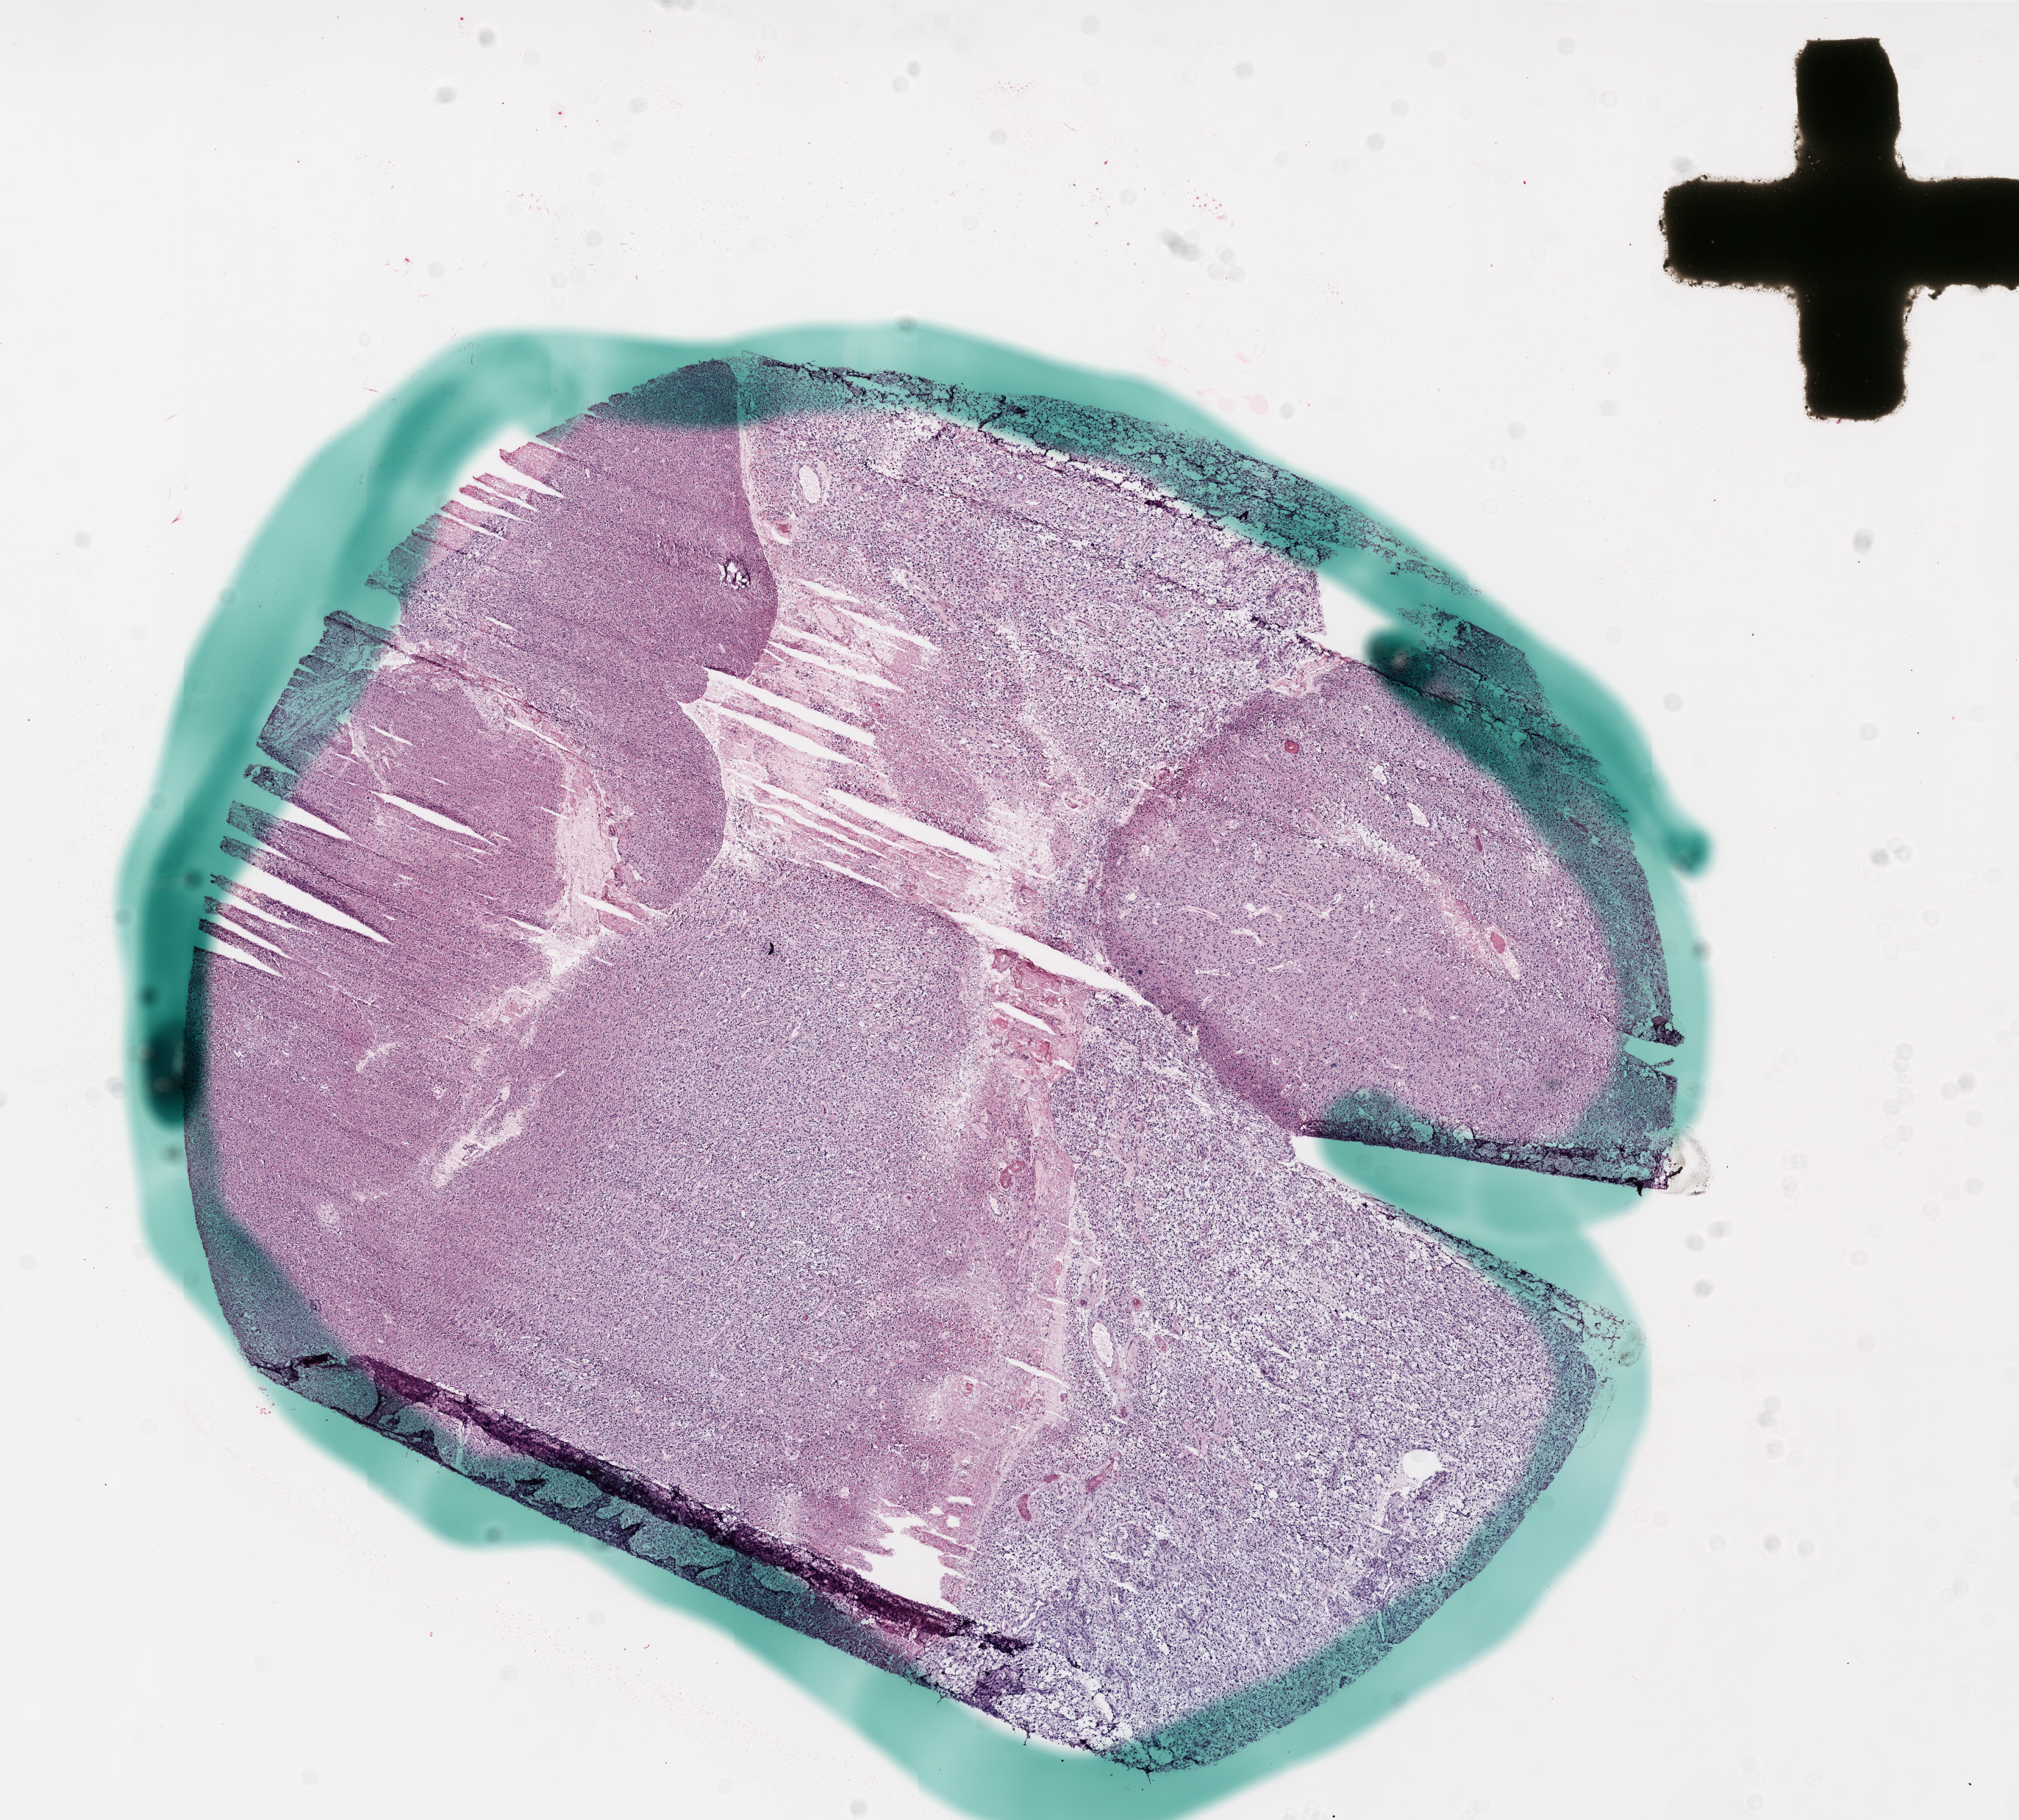
H&E whole-slide image, low-resolution overview of the scanned area, about 11.0 x 9.9 mm; frozen section; sample: primary tumour, brain. Male patient; age at initial diagnosis 67 years. Composition of this section per pathologist review: tumour cells 85%, tumour nuclei 95%, normal cells 5%, stromal cells 0%, necrosis 10%.
Histologic diagnosis: Glioblastoma.